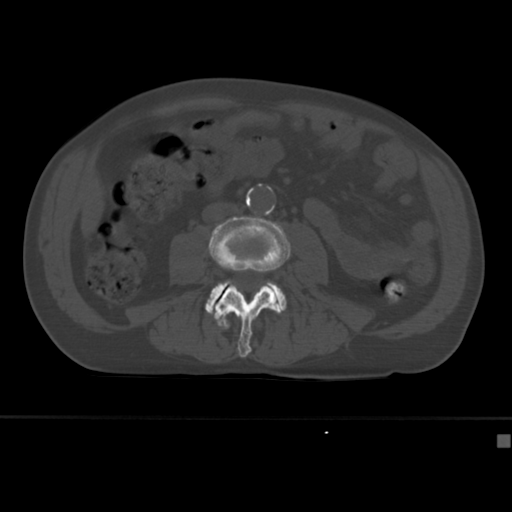
CT including the spine, one axial slice; position 120 of 430 along the scan axis; reconstruction kernel Br40s; 120 kVp; bone window (W 1800 / L 400 HU); 1.5 mm slice thickness; 512 × 512 image matrix, field of view 337 × 337 mm. Male patient, age 64 years. From the clinical record (not read from this slice): primary cancer: uterus.
Structures marked on this image (semi-automatic segmentation, software-assisted and operator-edited):
- L3 vertebra: box from (x=209, y=216) to (x=291, y=358) px
- L4 vertebra: (x=205, y=280)–(x=287, y=314)